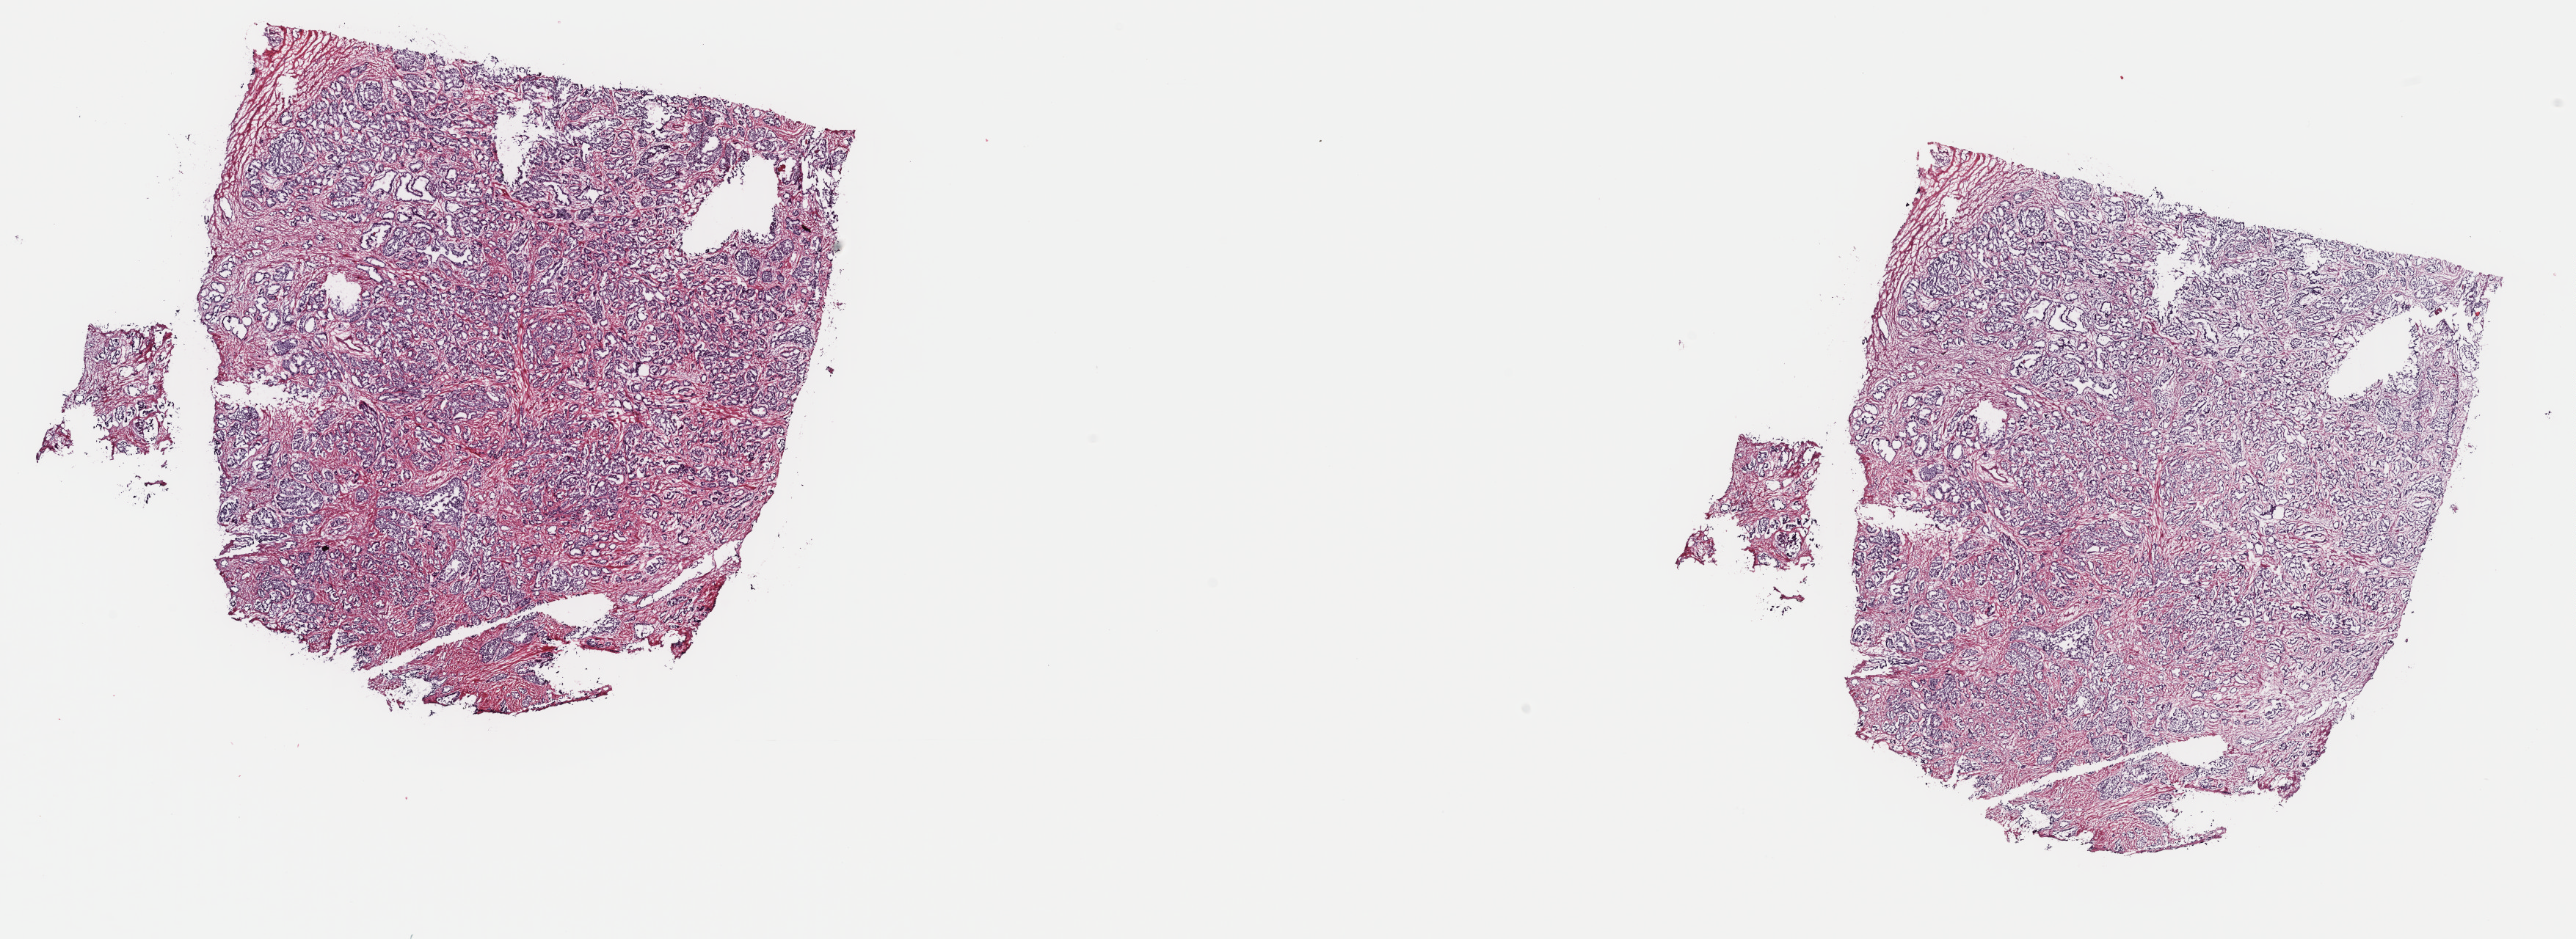
Digitized H&E-stained tissue section (whole slide) — low-resolution overview of the scanned area, about 27.7 x 10.1 mm (from a 40x scan), frozen section, primary tumour sample from the prostate. Patient: male, age at initial diagnosis 61 years. Gleason score: 7 (3+4). Pathologist review of this section (percent, as recorded): tumour cells 65%, tumour nuclei 85%, normal cells 0%, stromal cells 33%, necrosis 2%. Infiltration values recorded for this section: lymphocyte infiltration 3%, monocyte infiltration 0%, neutrophil infiltration 0%.
• histologic diagnosis: Adenocarcinoma, NOS (prostate gland)
• laterality: bilateral